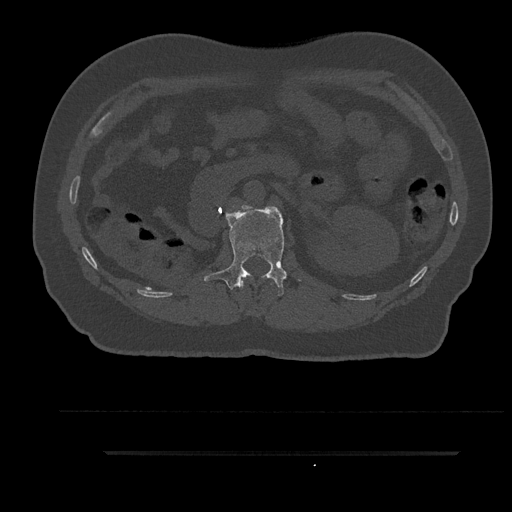
CT including the spine, one axial slice; position 180 of 797 along the scan axis; reconstruction kernel Br40s/3; 120 kVp; bone window (W 1800 / L 400 HU); 512 × 512 image matrix, field of view 432 × 432 mm. Patient: male, 63 years. From the clinical record (not read from this slice): primary cancer: renal; vertebrae with lytic lesions (as recorded): T8.
Annotated regions visible in this slice (semi-automatically segmented with operator editing):
- L1 vertebra: bounding box <204,206,286,296> (left, top, right, bottom; pixels)
- T12 vertebra: <240,280,272,288>